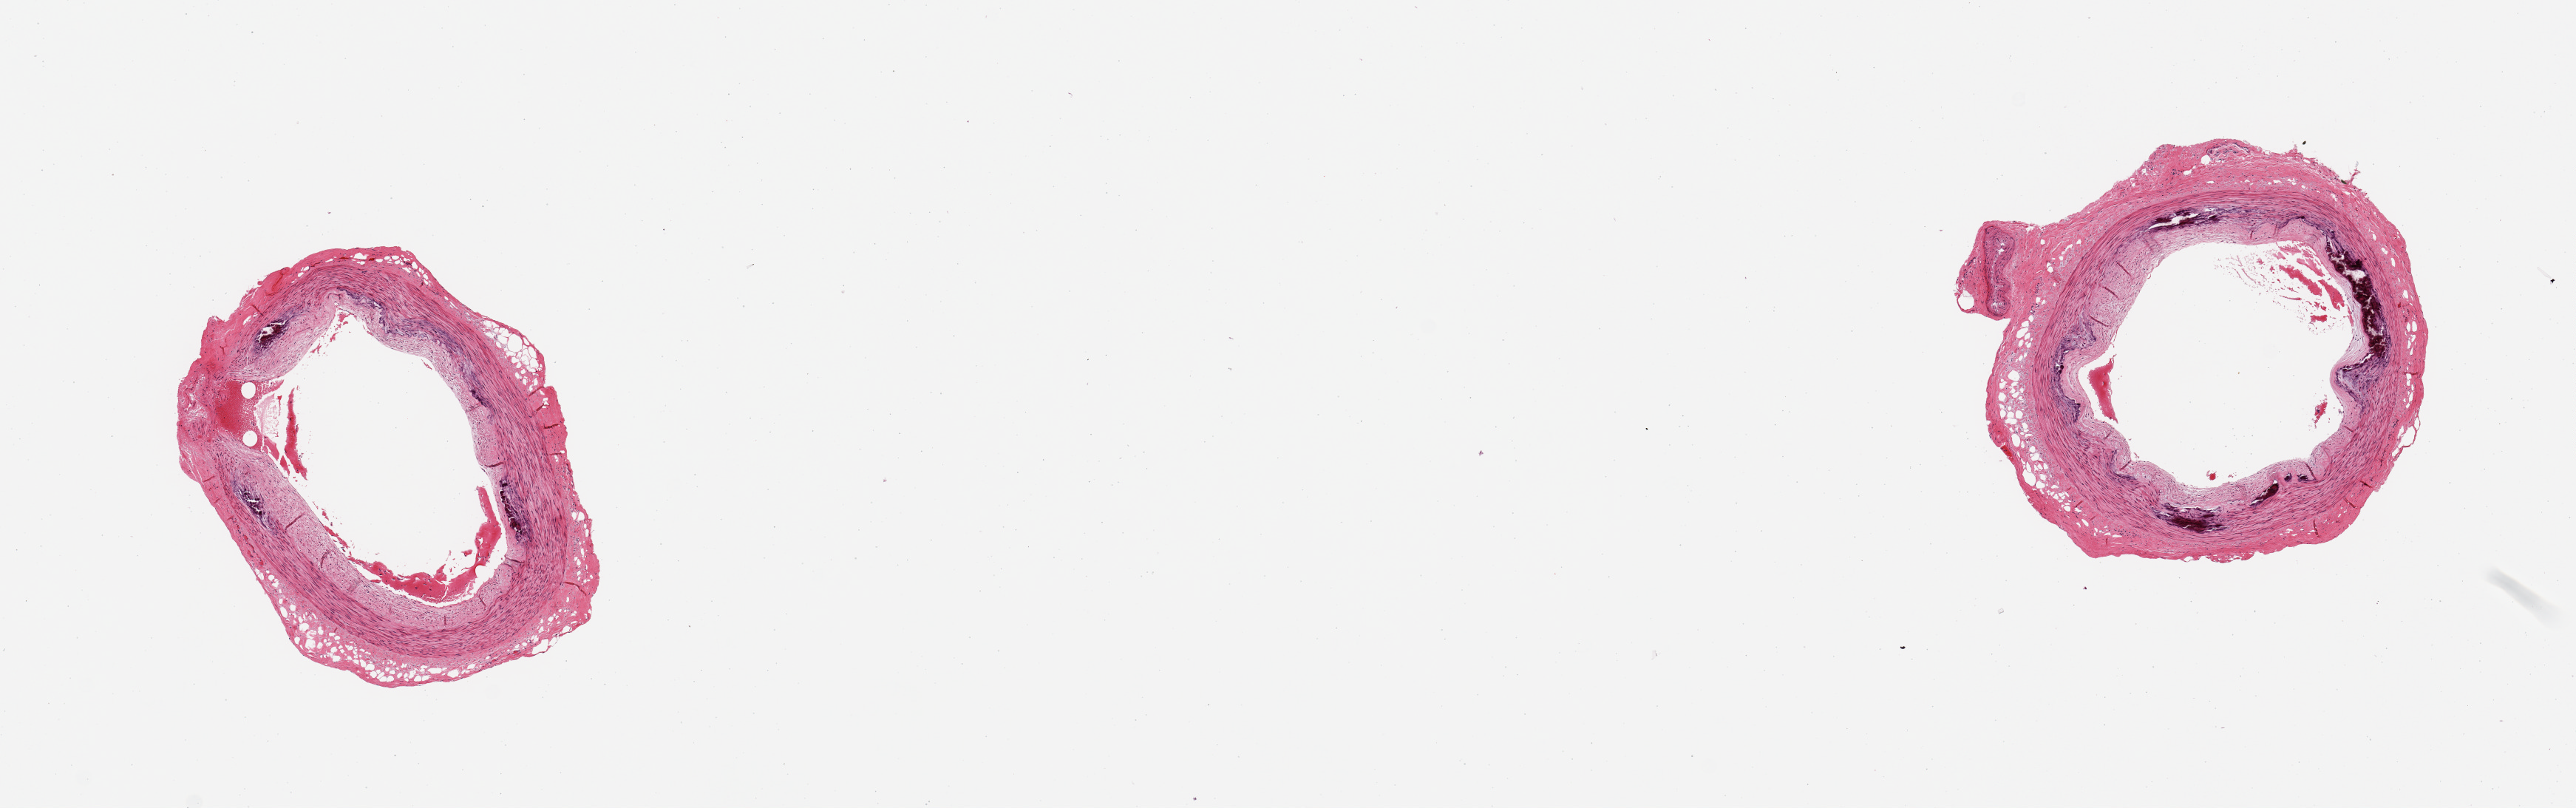
Whole-slide image, hematoxylin and eosin (H&E) stain — whole scanned area (about 13.8 x 4.3 mm) shown as a low-resolution overview, PAXgene-fixed, paraffin-embedded tissue, sampled site (target tissue): tibial artery, tissue donor sample. Donor sex: male.
- reviewer comment on this tissue sample: 2 pieces; atheroslerosis and medial calcification